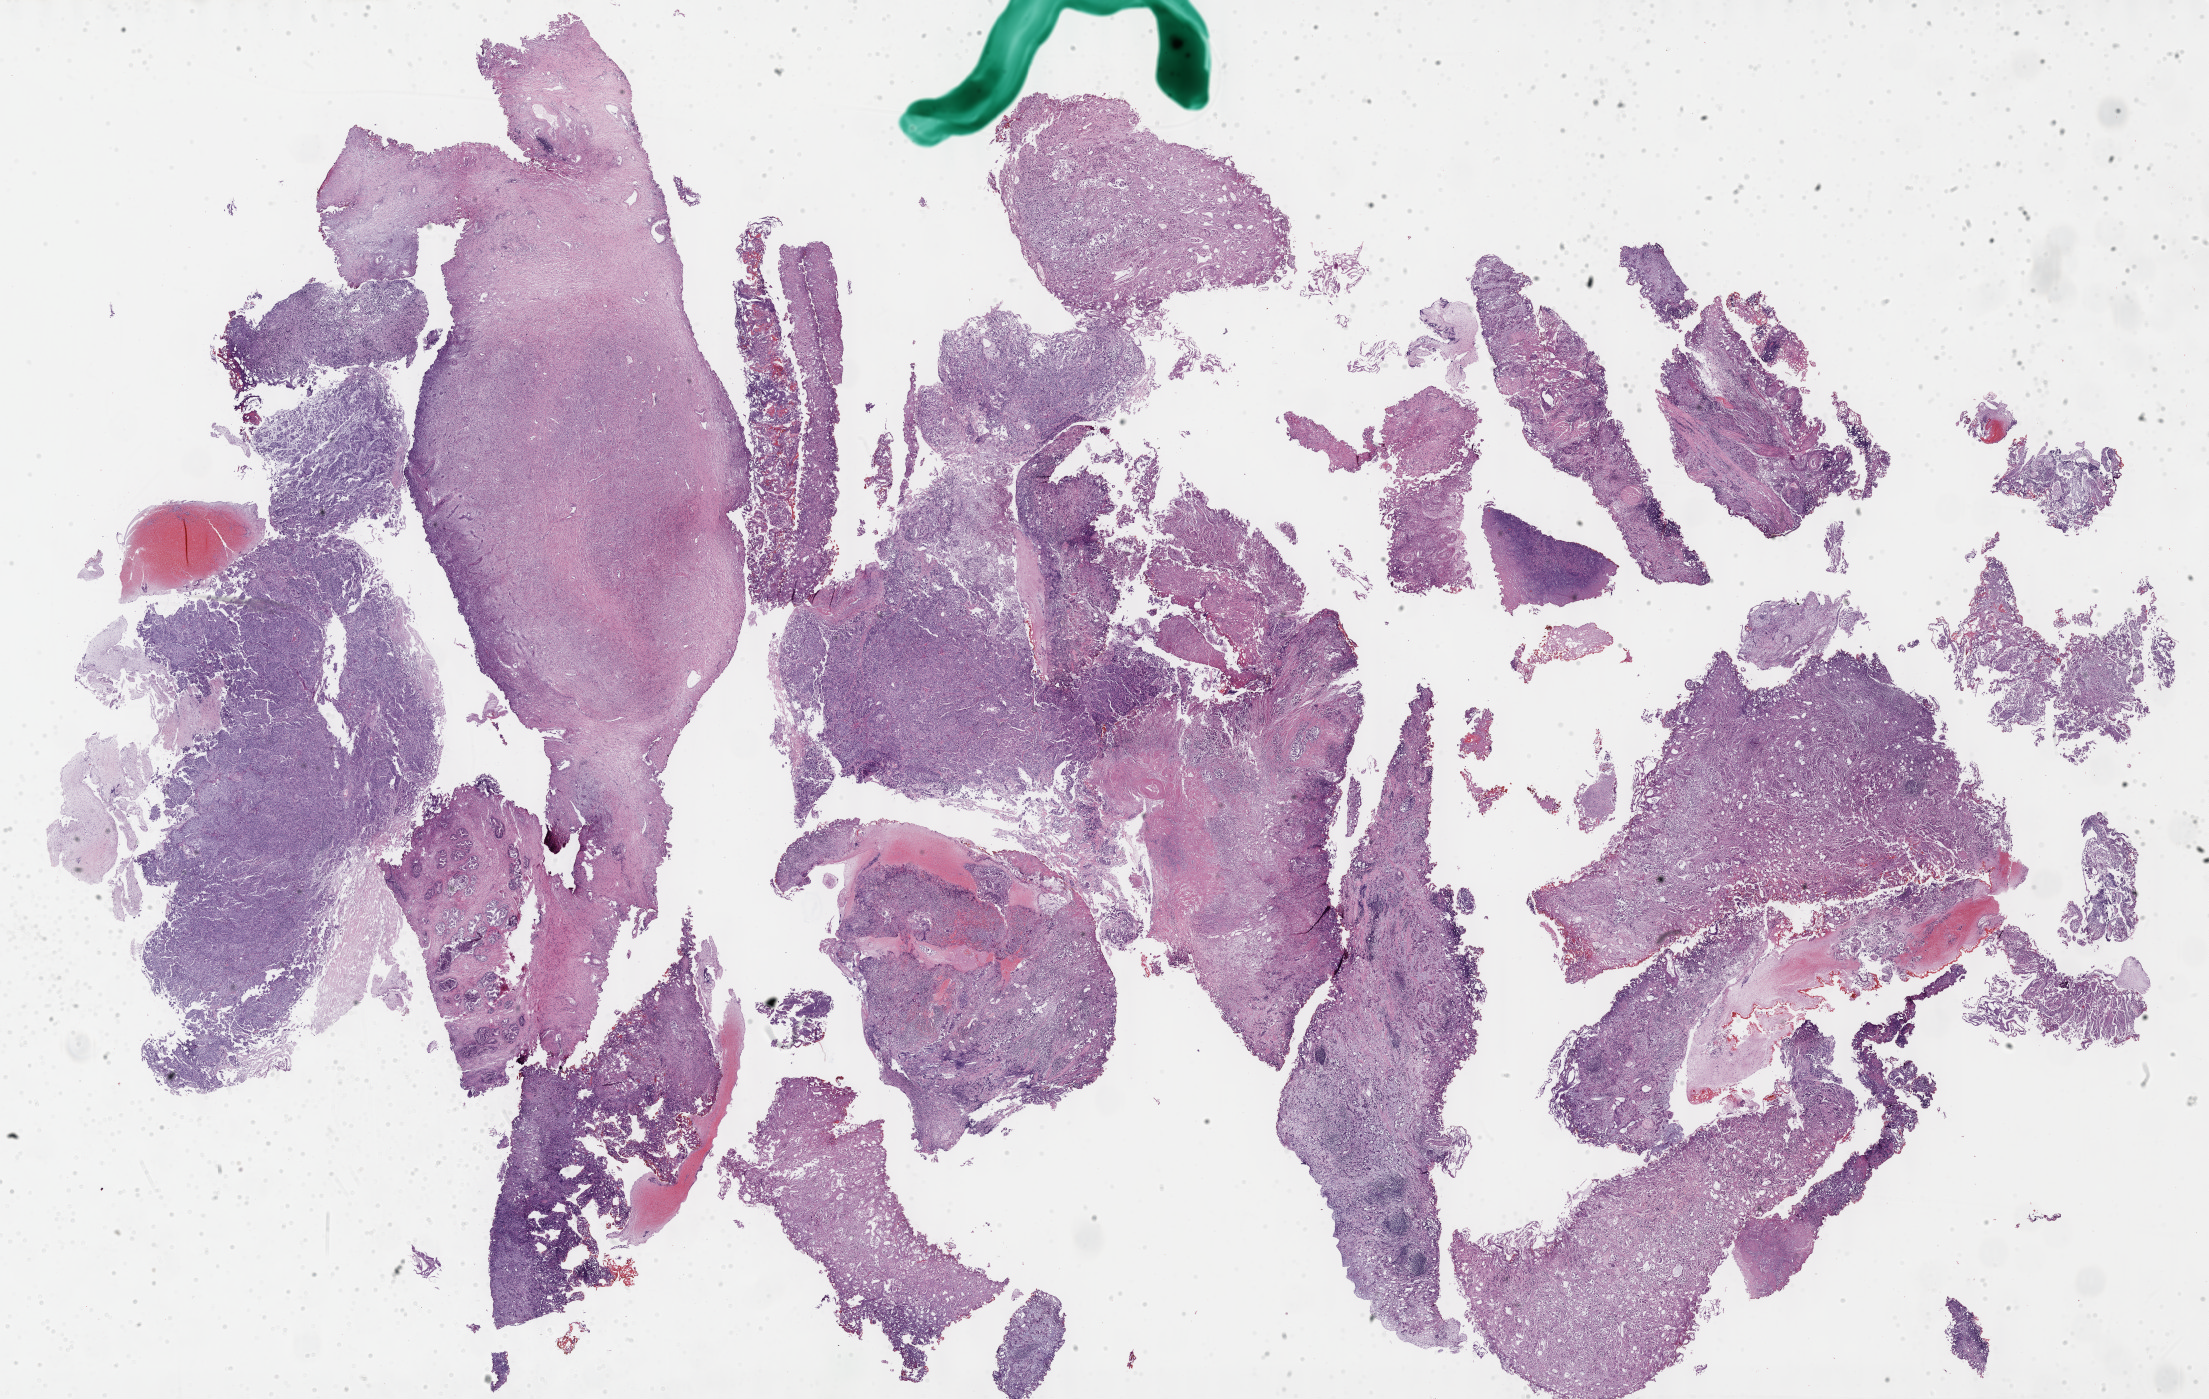
Whole-slide histology image, H&E-stained — shown as a low-resolution overview of the whole scanned area (about 35.7 x 22.6 mm), formalin-fixed paraffin-embedded (FFPE) diagnostic section, primary tumour sample from the bladder. Male patient; age at initial diagnosis 77 years. Histologic grade: high grade.
* pathologic diagnosis: Transitional cell carcinoma
* AJCC pathologic stage: IV (7th edition)
* lymph nodes positive (case pathology): 1 of 28 examined